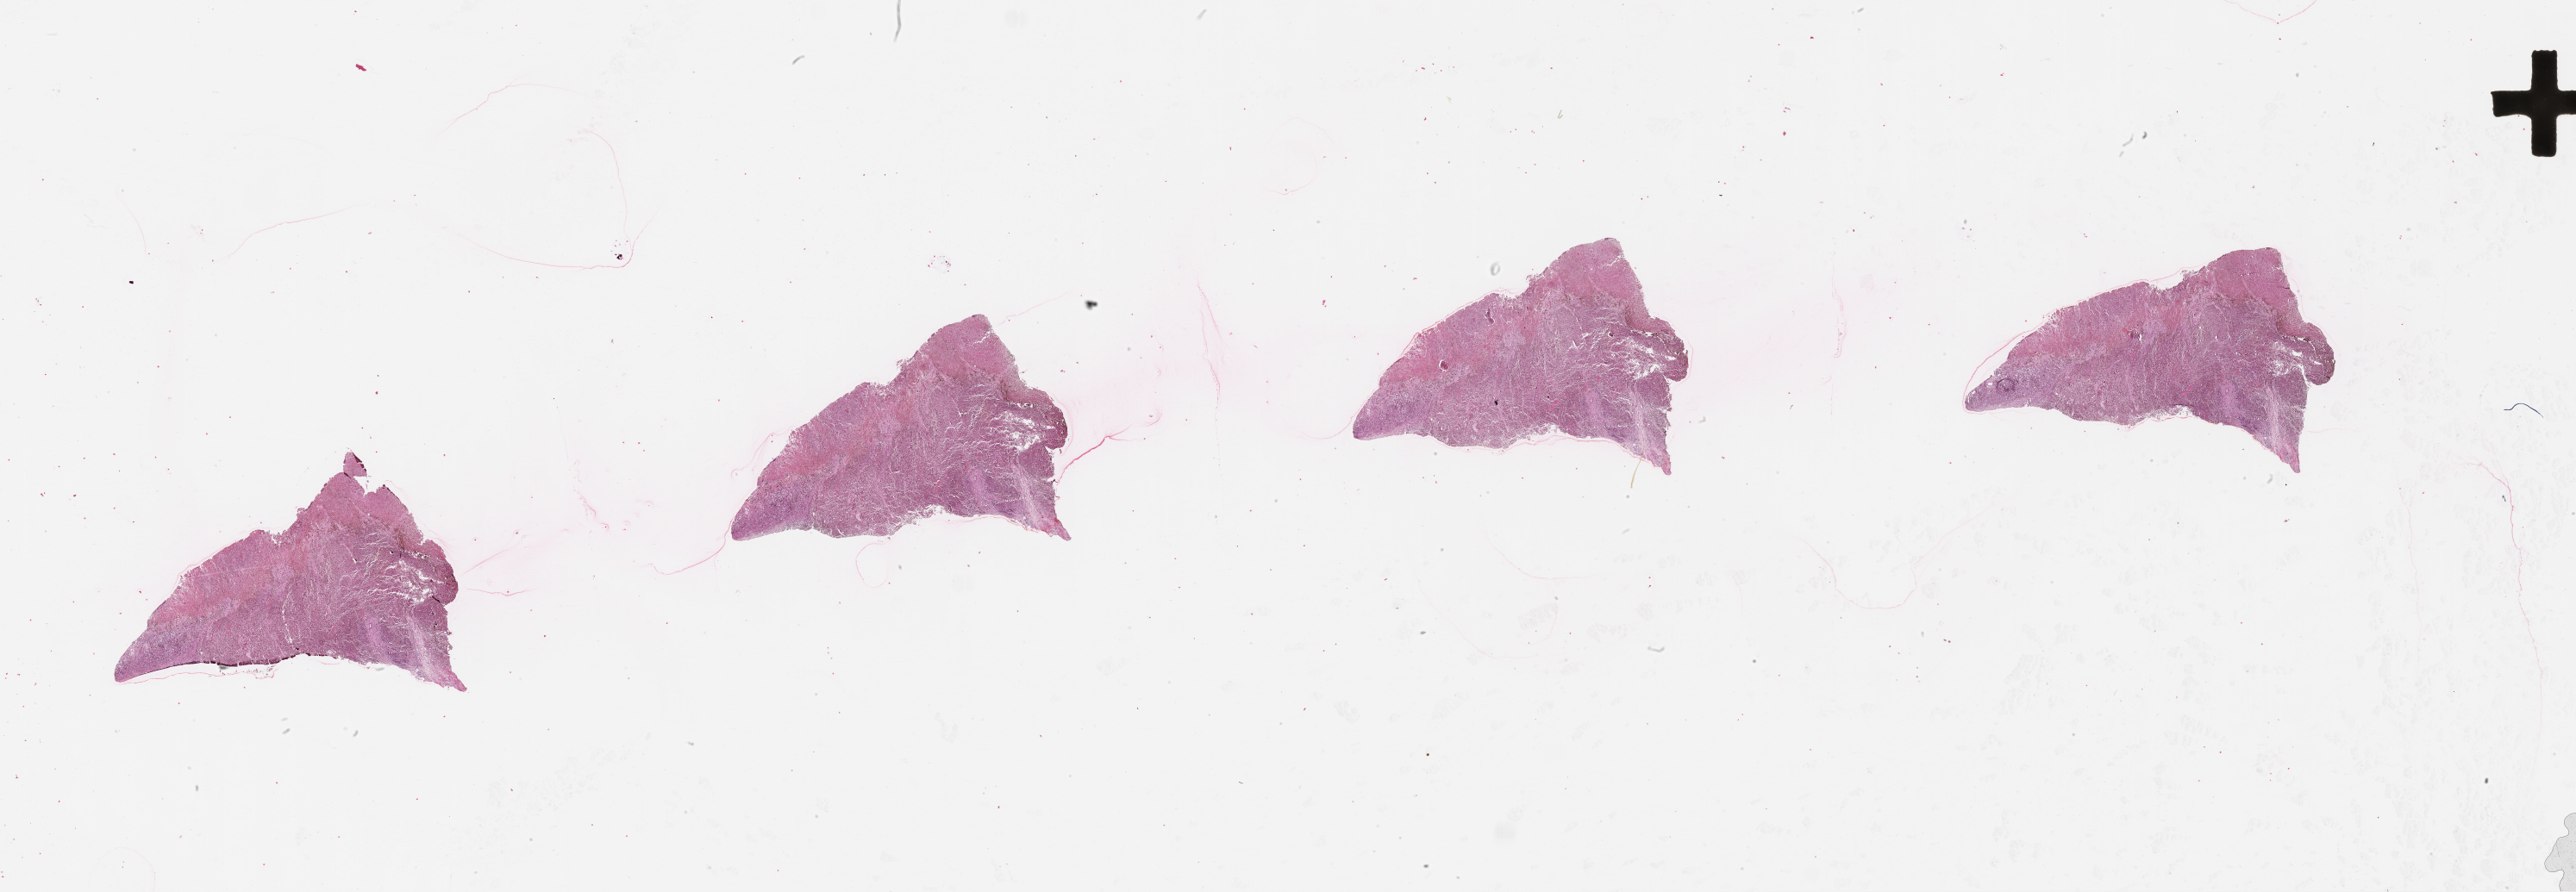
Hematoxylin and eosin (H&E) stained whole-slide image — low-resolution overview of the scanned area, about 48.1 x 16.7 mm (slide scanned at 20x). Female, 76 y/o.
* patient diagnosis: Malignant melanoma, NOS